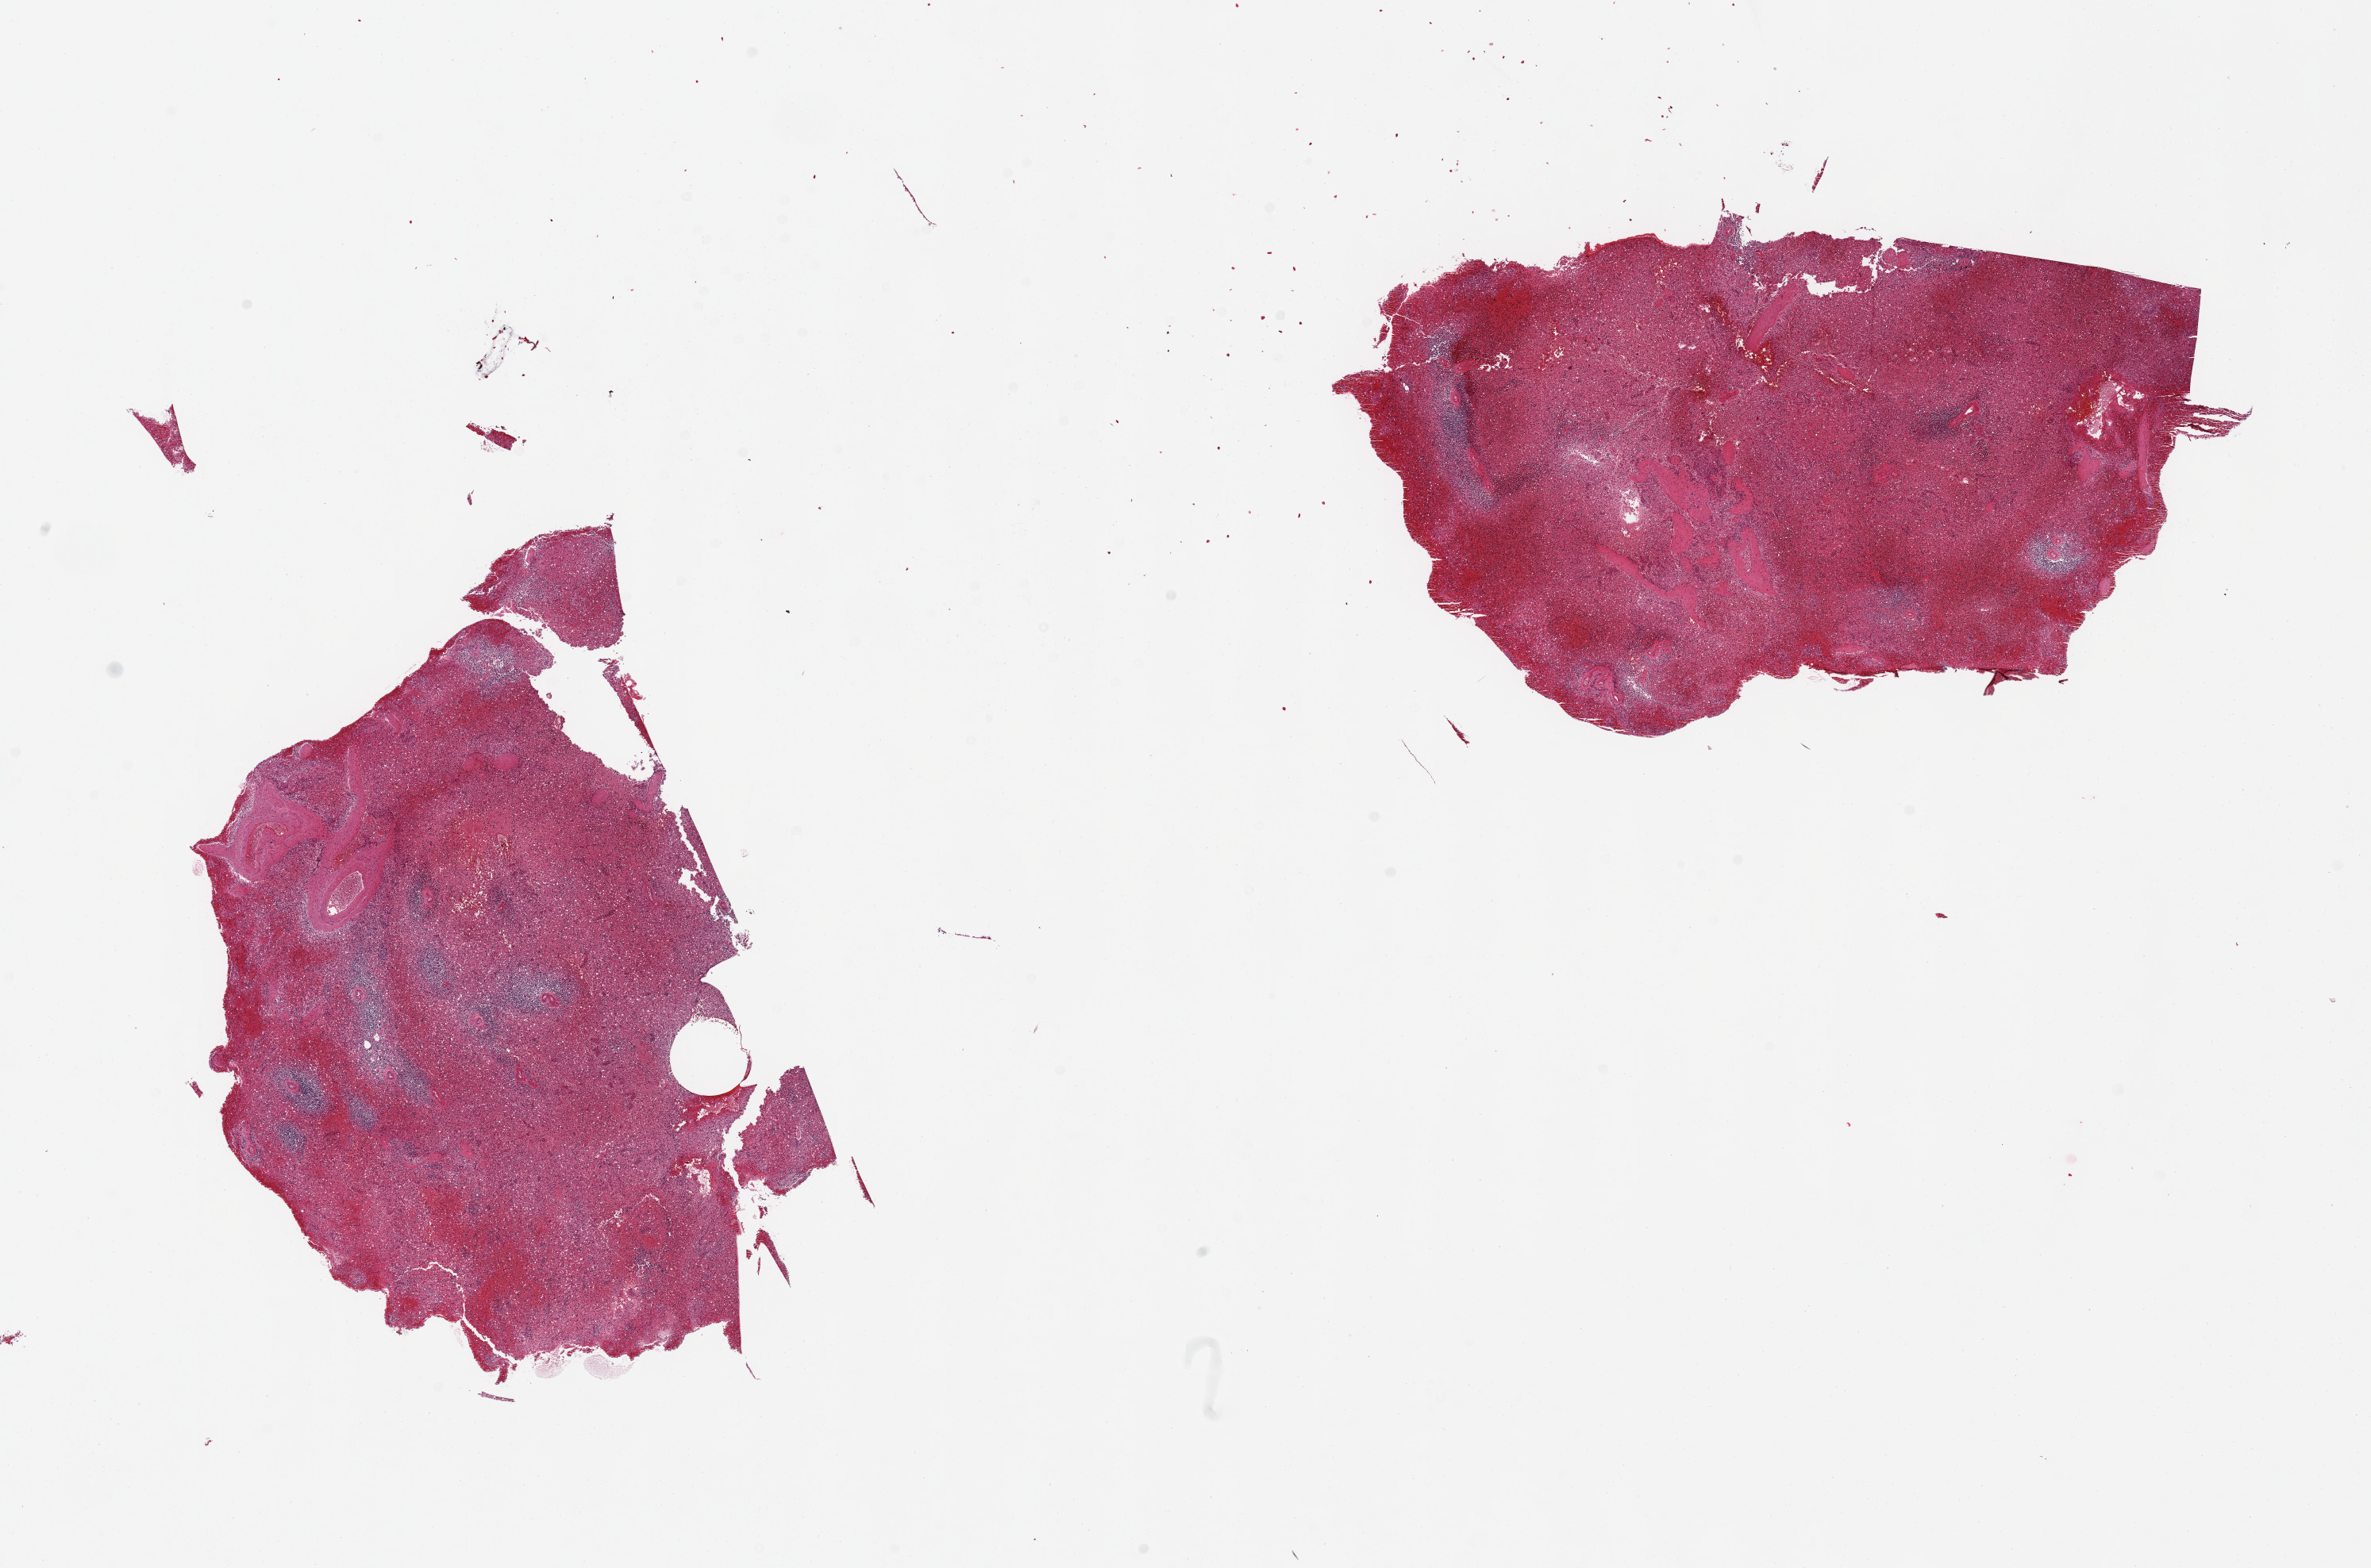
Digitized hematoxylin and eosin (H&E)-stained section, shown as a low-resolution overview of the whole scanned area (about 23.6 x 15.6 mm, acquisition: 20x scan), PAXgene-fixed paraffin-embedded (PFPE) section, sampled site (target tissue): spleen, donor tissue sample. Donor sex: male.
Pathologist's review note for this sample: 2 pieces, 7x5.5 and 8.5x5mm; moderate congestion.